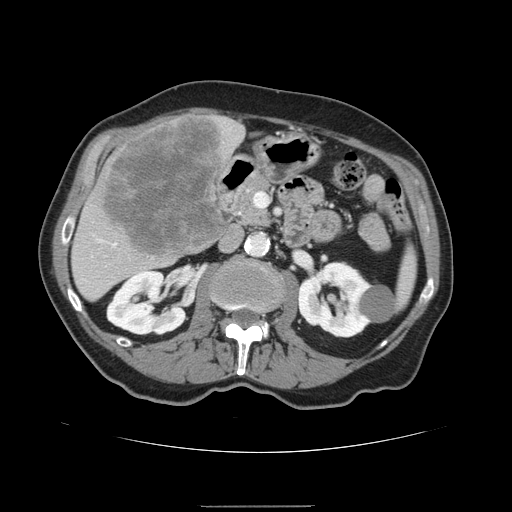
Contrast-enhanced abdominal CT, one axial slice. Position 65 of 168 along the scan axis. Soft-tissue window (W 400 / L 40 HU). 2.5 mm slice thickness. 512 × 512 image matrix, field of view 386 × 386 mm. Male patient, age 74 years. From the clinical record (not read from this slice): diagnosis: colorectal cancer liver metastases, imaged before liver resection; multiple liver metastases: no.
Structures marked on this image (outlined manually by an expert reader):
- liver: bounding box <71,114,246,302> (left, top, right, bottom; pixels)
- planned liver remnant (the part of the liver to remain after resection): <79,284,105,301>
- liver metastasis: <103,118,229,258>